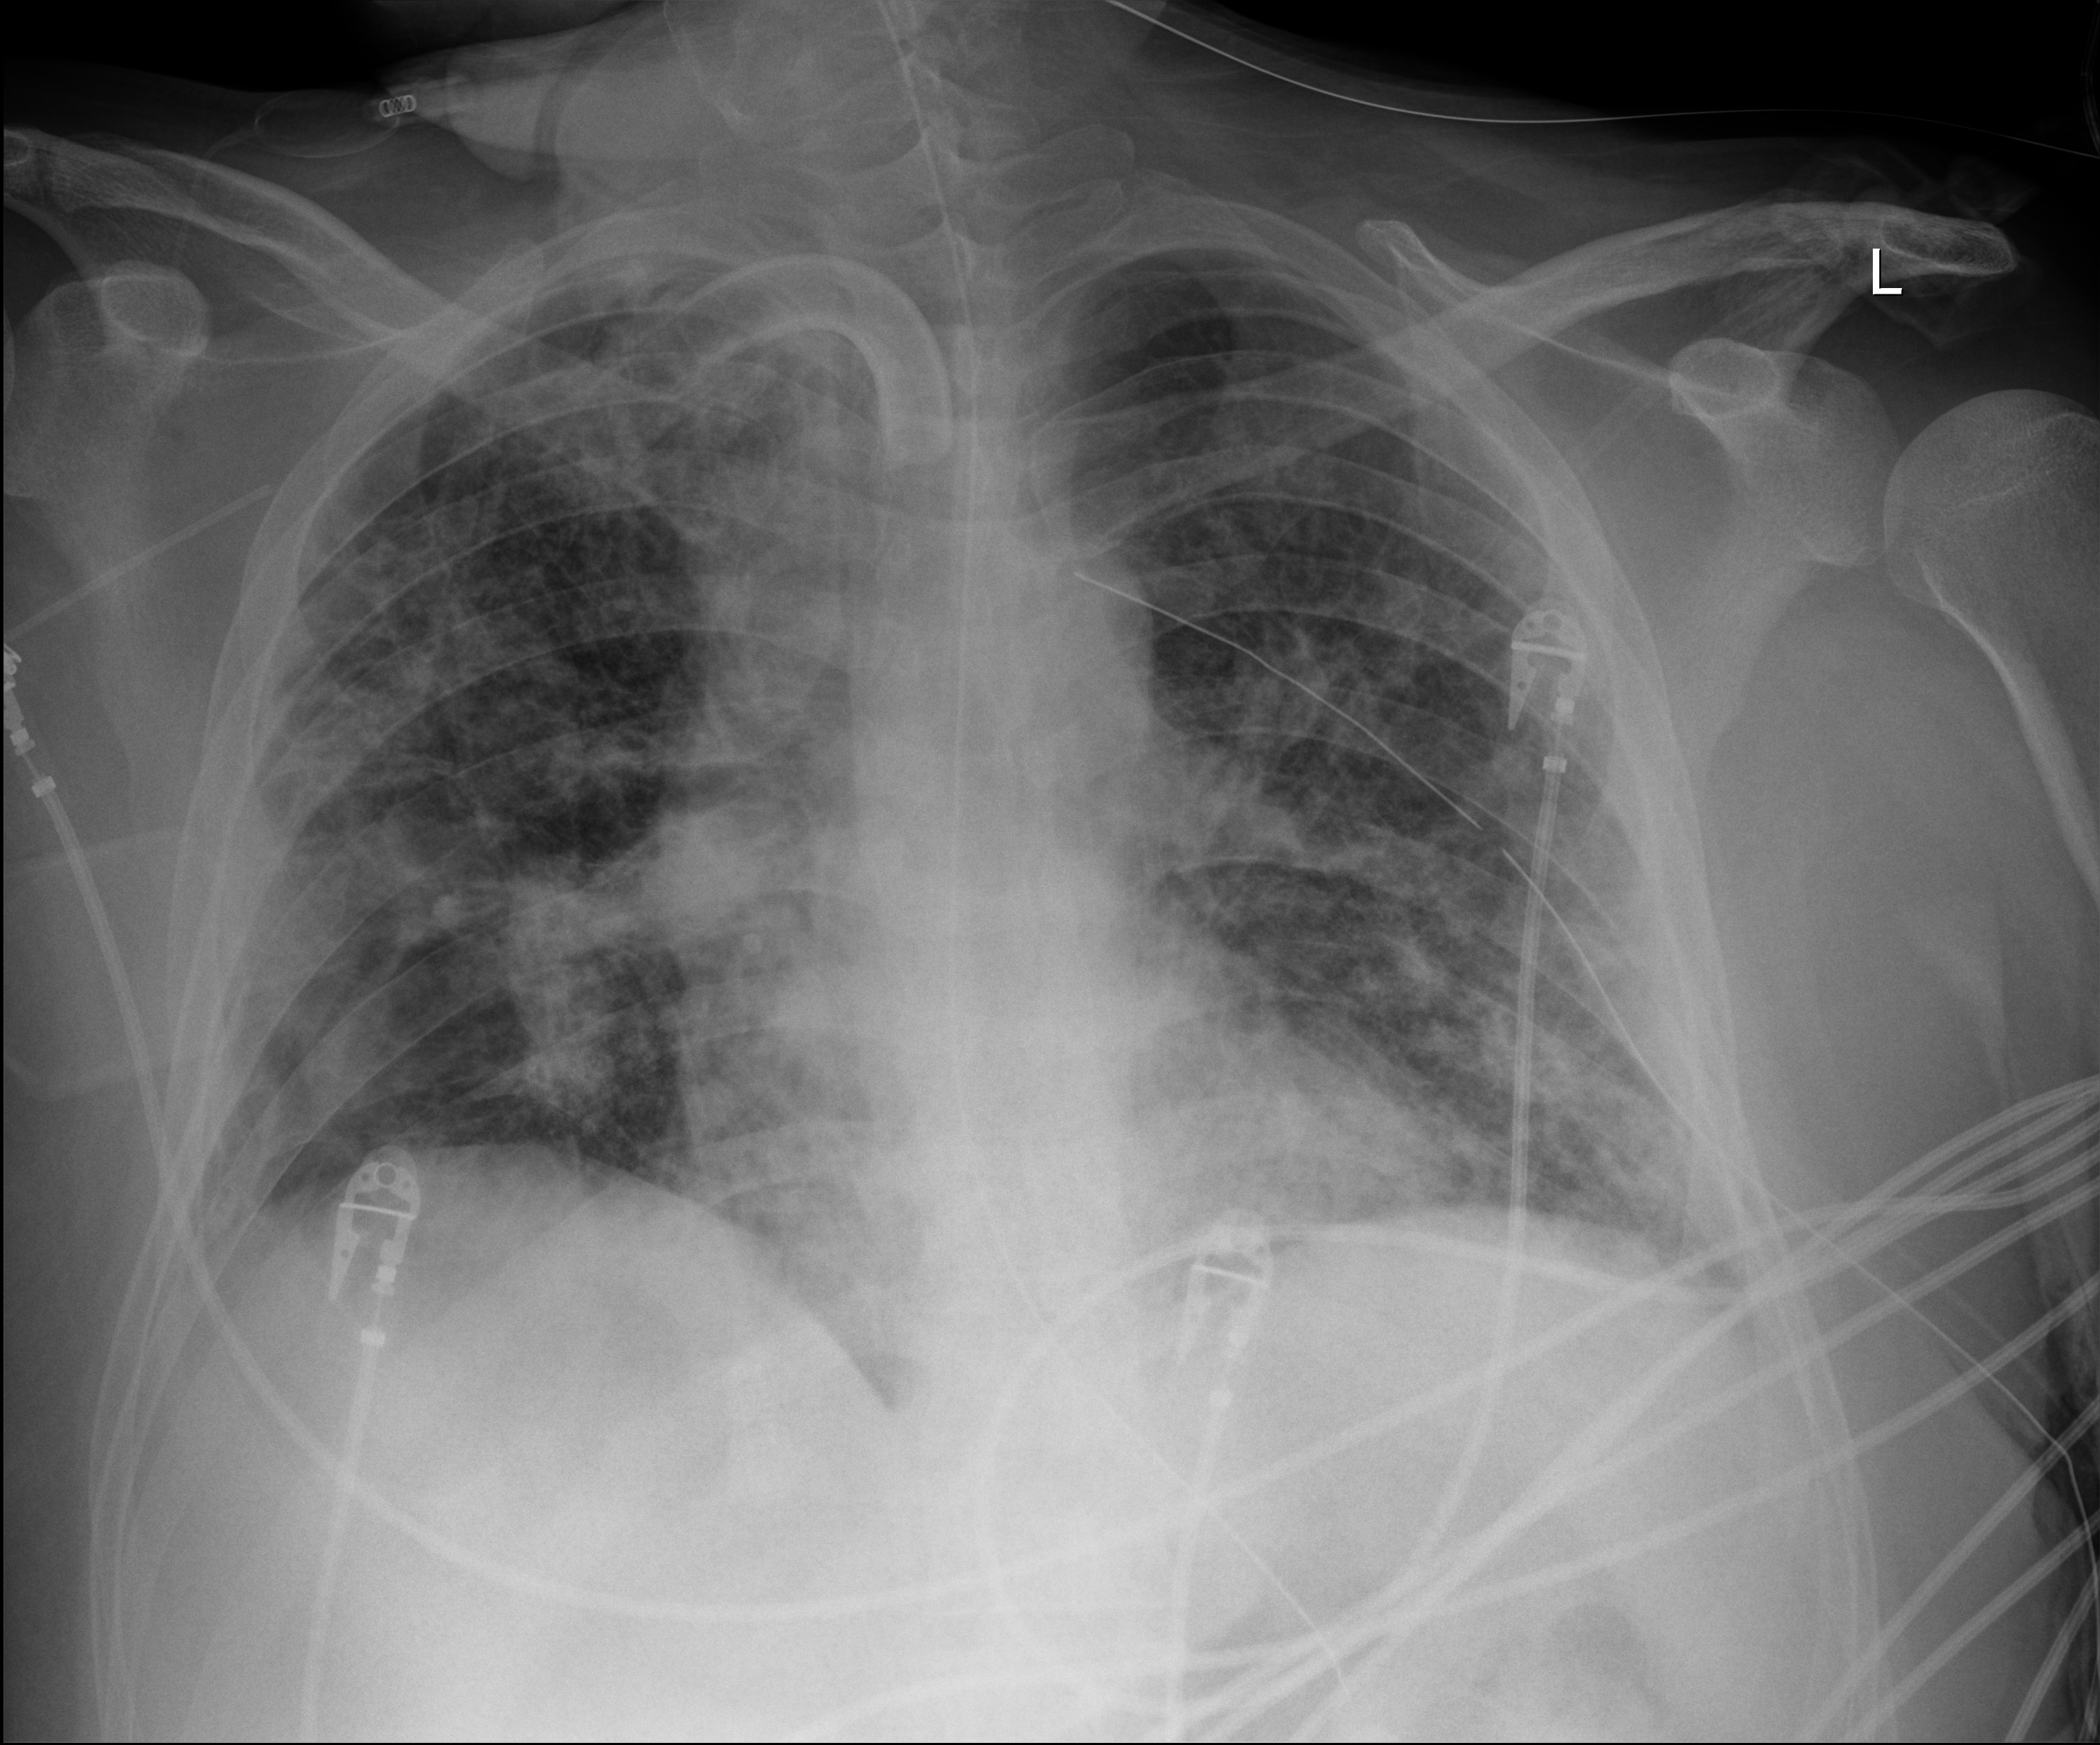
Chest X-ray (portable), anteroposterior (AP) projection. Patient hospitalised with COVID-19; male, aged 18–59 years.
Hospital-stay facts (about this admission, not read from this image; timing relative to this image not recorded):
- admitted to intensive care during this hospital stay: yes